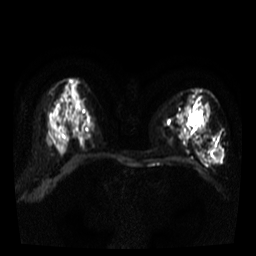
Breast MRI, one axial slice. Position 23 of 38 along the scan axis. Diffusion-weighted series; image 2 of 4 stored at this slice position (different b-values; order by instance number). 3 T. 5 mm slice thickness. 256 × 256 image matrix, field of view 320 × 320 mm. Female patient.
Annotated regions visible in this slice (manually delineated by an expert):
- tumour on diffusion-weighted imaging: box from (x=212, y=149) to (x=223, y=160) px